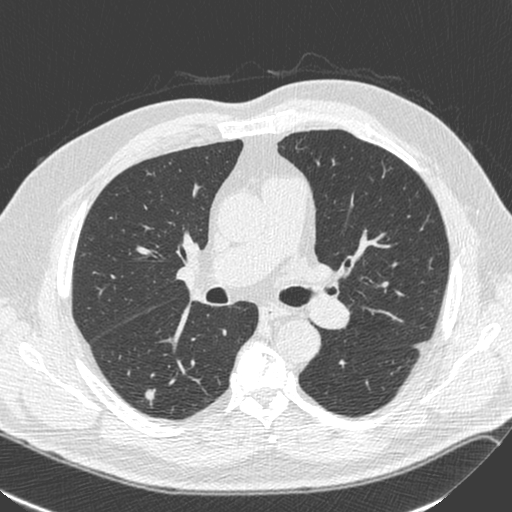
Axial slice from a low-dose chest CT screening exam; first (baseline) screen; lung window (W 1500 / L -600 HU); 1.3 mm slice thickness; 512 × 512 image matrix, field of view 357 × 357 mm. Male, age 71 years at enrolment. Former smoker at enrolment.
Lesion marked by an expert reader, bounding box [x1, y1, x2, y2] px = [138, 381, 170, 408]. Reader record for this screening exam (exam-level; its link to the box is not recorded): non-calcified nodule or mass ≥4 mm, right lower lobe, 6 × 6 mm, smooth margins, soft tissue attenuation. Lung cancer was diagnosed 231 days after this screen: squamous cell carcinoma, NOS, right lower lobe, poorly differentiated (G3), stage IA (AJCC 6th edition), 4 mm at pathology.